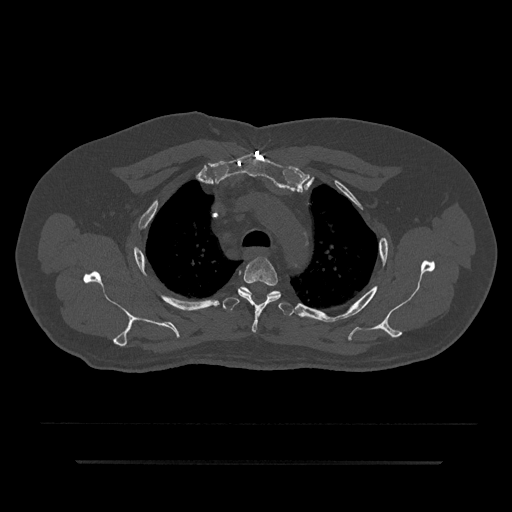
CT including the spine, one axial slice. Position 646 of 797 along the scan axis. Reconstruction kernel Br40s/3. 120 kVp. Bone window (W 1800 / L 400 HU). 0.5 mm slice thickness. 512 × 512 image matrix, field of view 464 × 464 mm. Patient: male, 59 years. Case-level facts recorded for this patient, not image findings: primary cancer: bile ducts; vertebrae with lytic lesions (as recorded): T10.
Outlined on this slice (semi-automatic segmentation, software-assisted and operator-edited):
- T3 vertebra: bounding box <238,257,281,332> (left, top, right, bottom; pixels)
- T4 vertebra: <223,287,295,316>